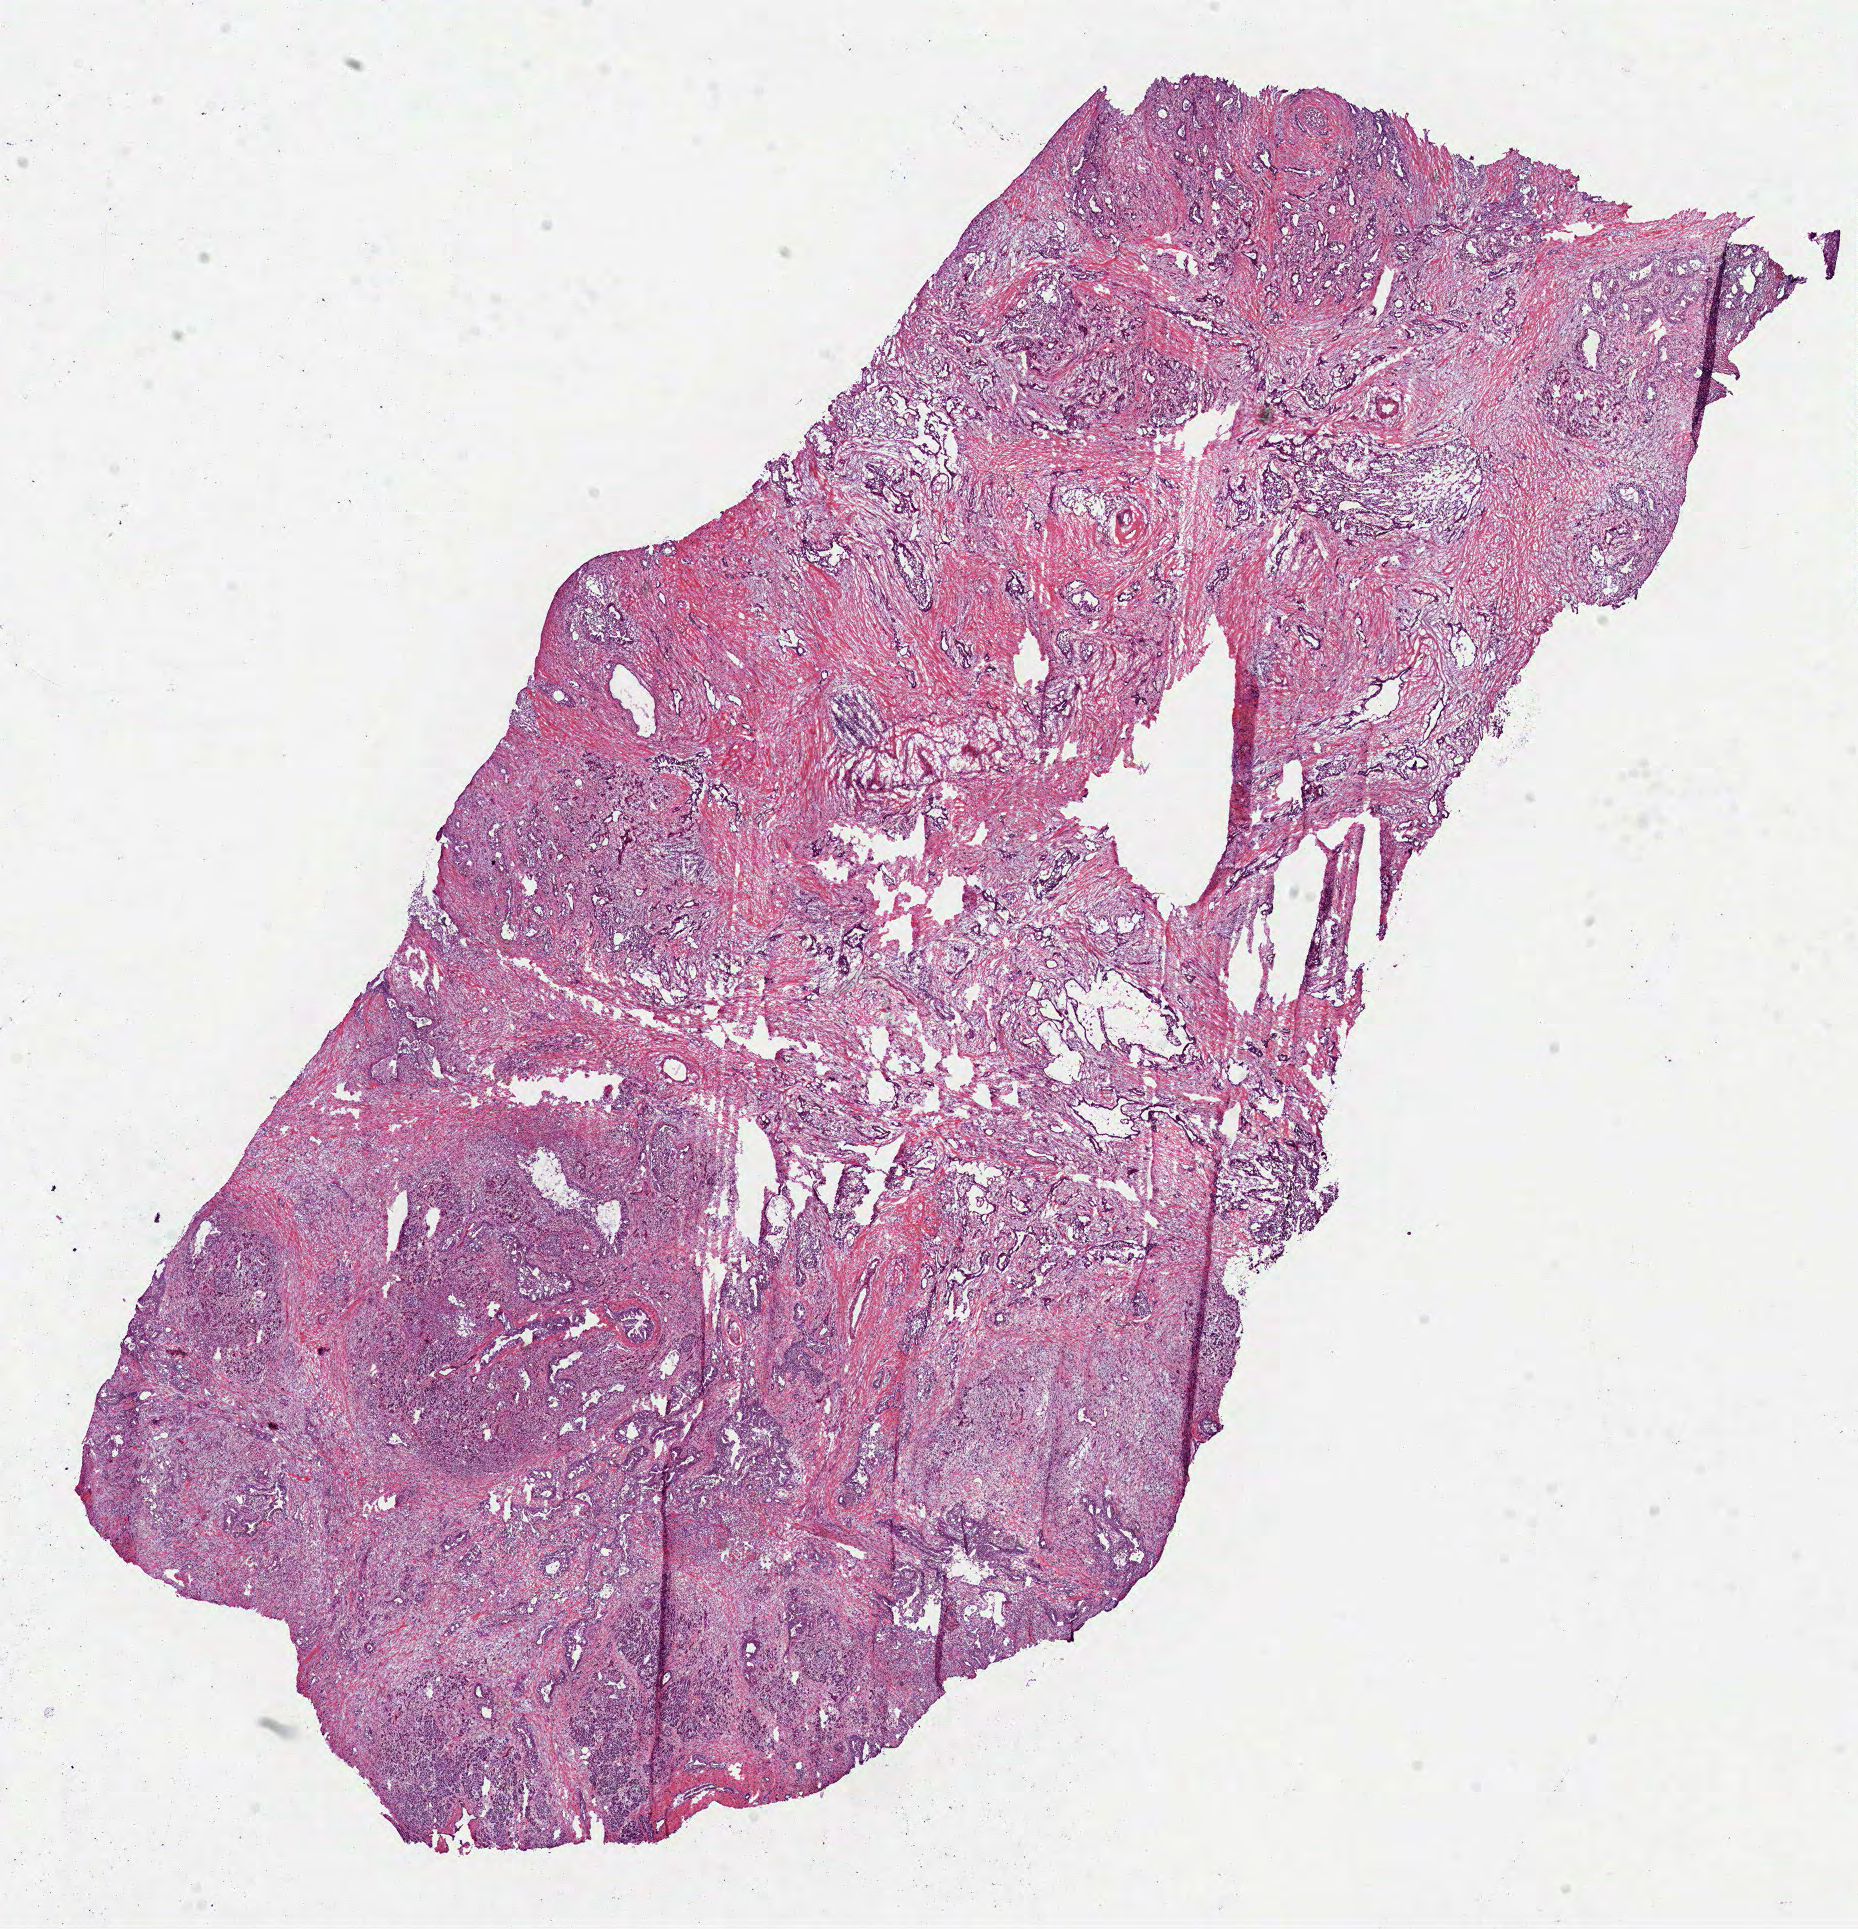
H&E-stained whole-slide image, shown as a low-resolution overview of the whole scanned area (about 15.0 x 15.6 mm, acquisition: 40x scan), frozen section from the top of the tissue portion, sample: primary tumour, pancreas. Male patient; age at initial diagnosis 59 years. Histologic grade: G2 (moderately differentiated). Composition of this section per pathologist review: tumour cells 100%, tumour nuclei 71%, normal cells 0%, stromal cells 0%, necrosis 0%. Inflammatory infiltration, as recorded: lymphocyte infiltration 15%, monocyte infiltration 0%, neutrophil infiltration 0%.
AJCC pathologic stage: IIB. Diagnosis: Infiltrating duct carcinoma, NOS (head of pancreas). TNM: T3 N1 M0.